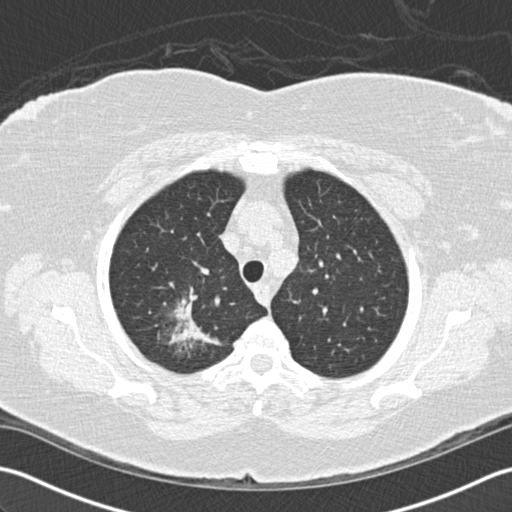
Low-dose screening chest CT, axial slice. Baseline screening round. Lung window (W 1500 / L -600 HU). 2 mm slice thickness. 120 kVp. 512 × 512 image matrix, field of view 350 × 350 mm. Female participant, aged 72 years at enrolment.
Expert reader's lesion annotation, bounding box [x1, y1, x2, y2] px = [137, 275, 232, 368]. The screening reader recorded 2 non-calcified nodules or masses ≥4 mm on this exam; which of them this box marks is not recorded. Participant outcome: lung cancer diagnosed 494 days after this screen — bronchiolo-alveolar adenocarcinoma, NOS, right upper lobe, stage IIIB (AJCC 6th edition), 45 mm at pathology.